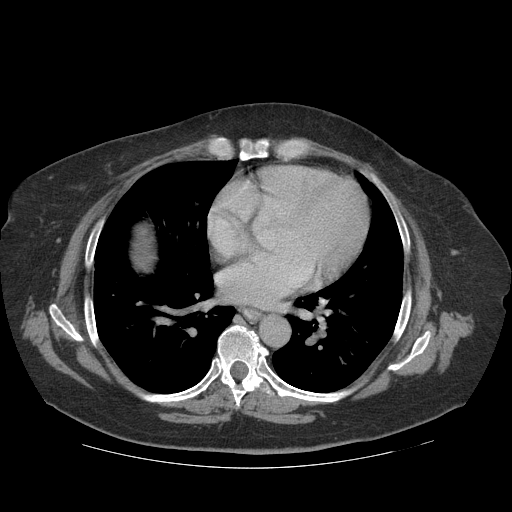
Contrast-enhanced abdominal CT (liver protocol), one axial slice. Position 114 of 121 along the scan axis. Reconstruction kernel STANDARD. 140 kVp. Soft-tissue window (W 400 / L 40 HU). 512 × 512 image matrix. Case-level facts recorded for this patient, not image findings: diagnosis: hepatocellular carcinoma (patient treated with transarterial chemoembolisation; whether this scan precedes or follows treatment is not stated here); TNM stage (as recorded): Stage-IIIA; Child-Pugh class: A; tumour differentiation: well differentiated; tumour nodularity: multinodular.
Annotated regions visible in this slice (semi-automatic segmentation, software-assisted and operator-edited):
- liver parenchyma outside the tumour (the mass and vessels are separate outlines, so this box may not span the whole liver): box from (x=132, y=224) to (x=156, y=268) px